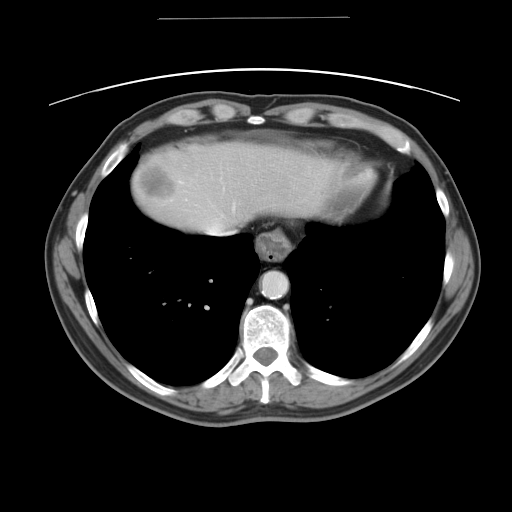
Contrast-enhanced abdominal CT, one axial slice; slice 43 of 49 in the series (ordered by position); reconstruction kernel STANDARD; 120 kVp; intravenous contrast given; soft-tissue window (W 400 / L 40 HU); 512 × 512 image matrix, field of view 413 × 413 mm. Male patient, age 57 years. From the clinical record (not read from this slice): diagnosis: colorectal cancer liver metastases, imaged before liver resection; multiple liver metastases: yes; largest metastasis: 4 cm.
Annotated regions visible in this slice (outlined manually by an expert reader):
- hepatic veins: bounding box (x1, y1, x2, y2) in pixels: (206, 206, 233, 233)
- liver: (130, 141, 334, 236)
- planned liver remnant (the part of the liver to remain after resection): (206, 141, 335, 236)
- liver metastasis: (137, 163, 179, 200)